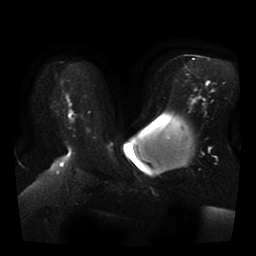
Breast MRI, one axial slice. Position 22 of 41 along the scan axis. Diffusion-weighted series; image 2 of 4 stored at this slice position (different b-values; order by instance number). 1.5 T. 5 mm slice thickness. 256 × 256 image matrix. Female patient.
Annotated regions visible in this slice (manually delineated by an expert):
- tumour on diffusion-weighted imaging: bounding box [x1, y1, x2, y2] px = [68, 111, 72, 116]